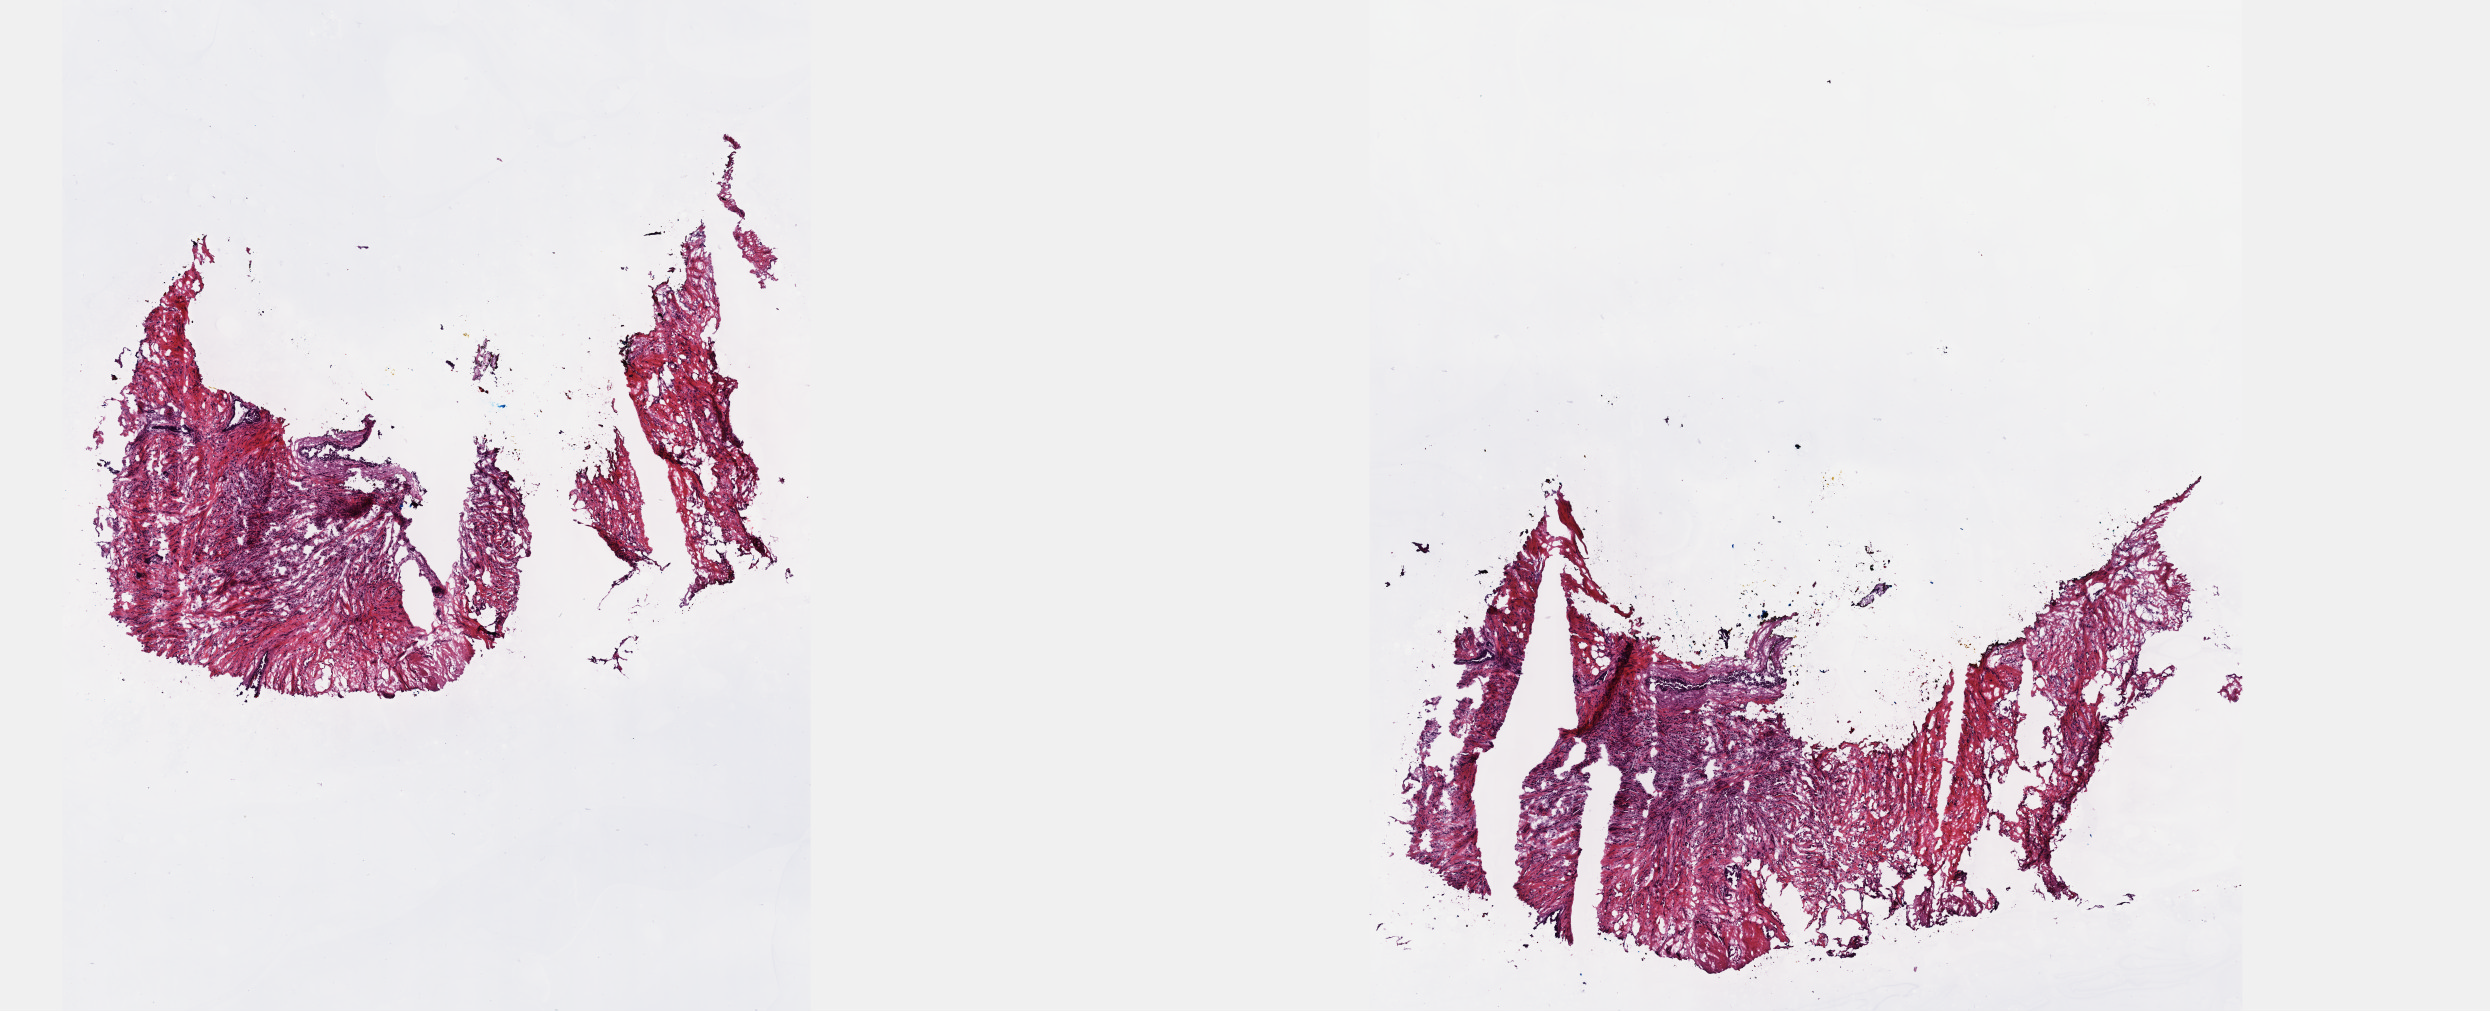
H&E whole-slide image, low-resolution overview of the scanned area, about 20.1 x 8.2 mm (from a 40x scan), frozen section from the top of the tissue portion, sample: primary tumour, breast. Patient: female, age at initial diagnosis 66 years. Pathologist review of this section (percent, as recorded): tumour cells 80%, tumour nuclei 80%, normal cells 0%, stromal cells 20%, necrosis 0%. Inflammatory infiltration, as recorded: lymphocyte infiltration 40%, monocyte infiltration 20%, neutrophil infiltration 20%.
Pathologic diagnosis: Lobular carcinoma, NOS. AJCC pathologic stage: IIA (7th edition).